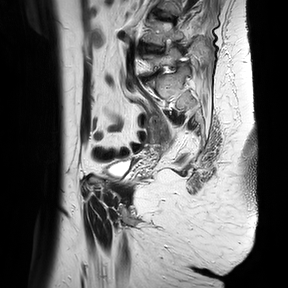
Pelvic MRI for cervical cancer, one sagittal slice; position 26 of 37 along the scan axis; T2-weighted; 1.5 T; TE 100 ms, TR 4174.1 ms; 288 × 288 image matrix, field of view 300 × 300 mm. Patient: female, 65 years.
Structures marked on this image (outlined manually by an expert reader):
- uterus and cervix: bounding box <148,114,170,145> (left, top, right, bottom; pixels)